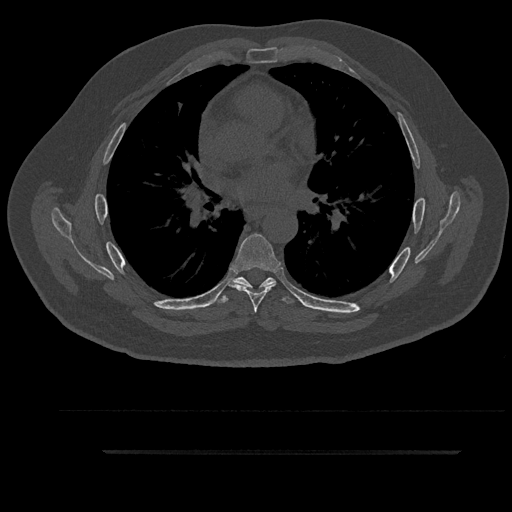
CT including the spine, one axial slice. Position 562 of 797 along the scan axis. 120 kVp. Bone window (W 1800 / L 400 HU). 0.5 mm slice thickness. 512 × 512 image matrix, field of view 432 × 432 mm. Male patient, age 63 years. Case-level facts recorded for this patient, not image findings: primary cancer: renal; vertebrae with lytic lesions (as recorded): T8.
Annotated regions visible in this slice (semi-automatic segmentation, software-assisted and operator-edited):
- T5 vertebra: bounding box (x1, y1, x2, y2) in pixels: (242, 277, 266, 291)
- T6 vertebra: (231, 234, 281, 313)
- T7 vertebra: (216, 277, 297, 304)